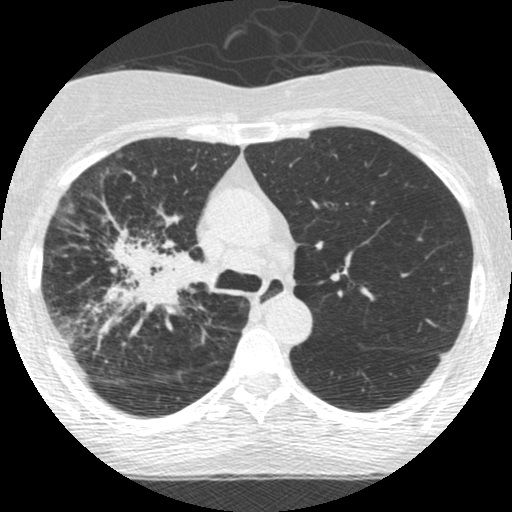
Low-dose screening chest CT, one axial slice; position 175 of 253 along the scan axis; 120 kVp; lung window (W 1500 / L -600 HU); 1.25 mm slice thickness; 512 × 512 image matrix.
Annotated regions visible in this slice (expert manual segmentation):
- lesion 2 (tumor, hilum of right lung): bounding box (x1, y1, x2, y2) in pixels: (99, 203, 210, 330)